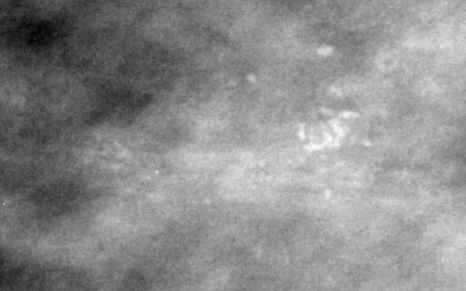
Cropped region of a digitized screen-film mammogram centred on a radiologist-marked abnormality; left breast; MLO view.
- Marked abnormality: calcifications, morphology pleomorphic, distribution clustered; BI-RADS assessment category 4; subtlety rating 3 on a 1 (subtle) to 5 (obvious) scale; pathology (as recorded): malignant.